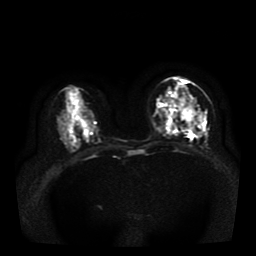
Breast MRI, one axial slice; slice 18 of 41 in the series (ordered by position); diffusion-weighted series; image 2 of 4 stored at this slice position (different b-values; order by instance number); 1.5 T; 5 mm slice thickness; 256 × 256 image matrix, field of view 330 × 330 mm. Female patient.
Outlined on this slice (expert manual segmentation):
- tumour on diffusion-weighted imaging: bounding box (x1, y1, x2, y2) in pixels: (173, 92, 203, 136)